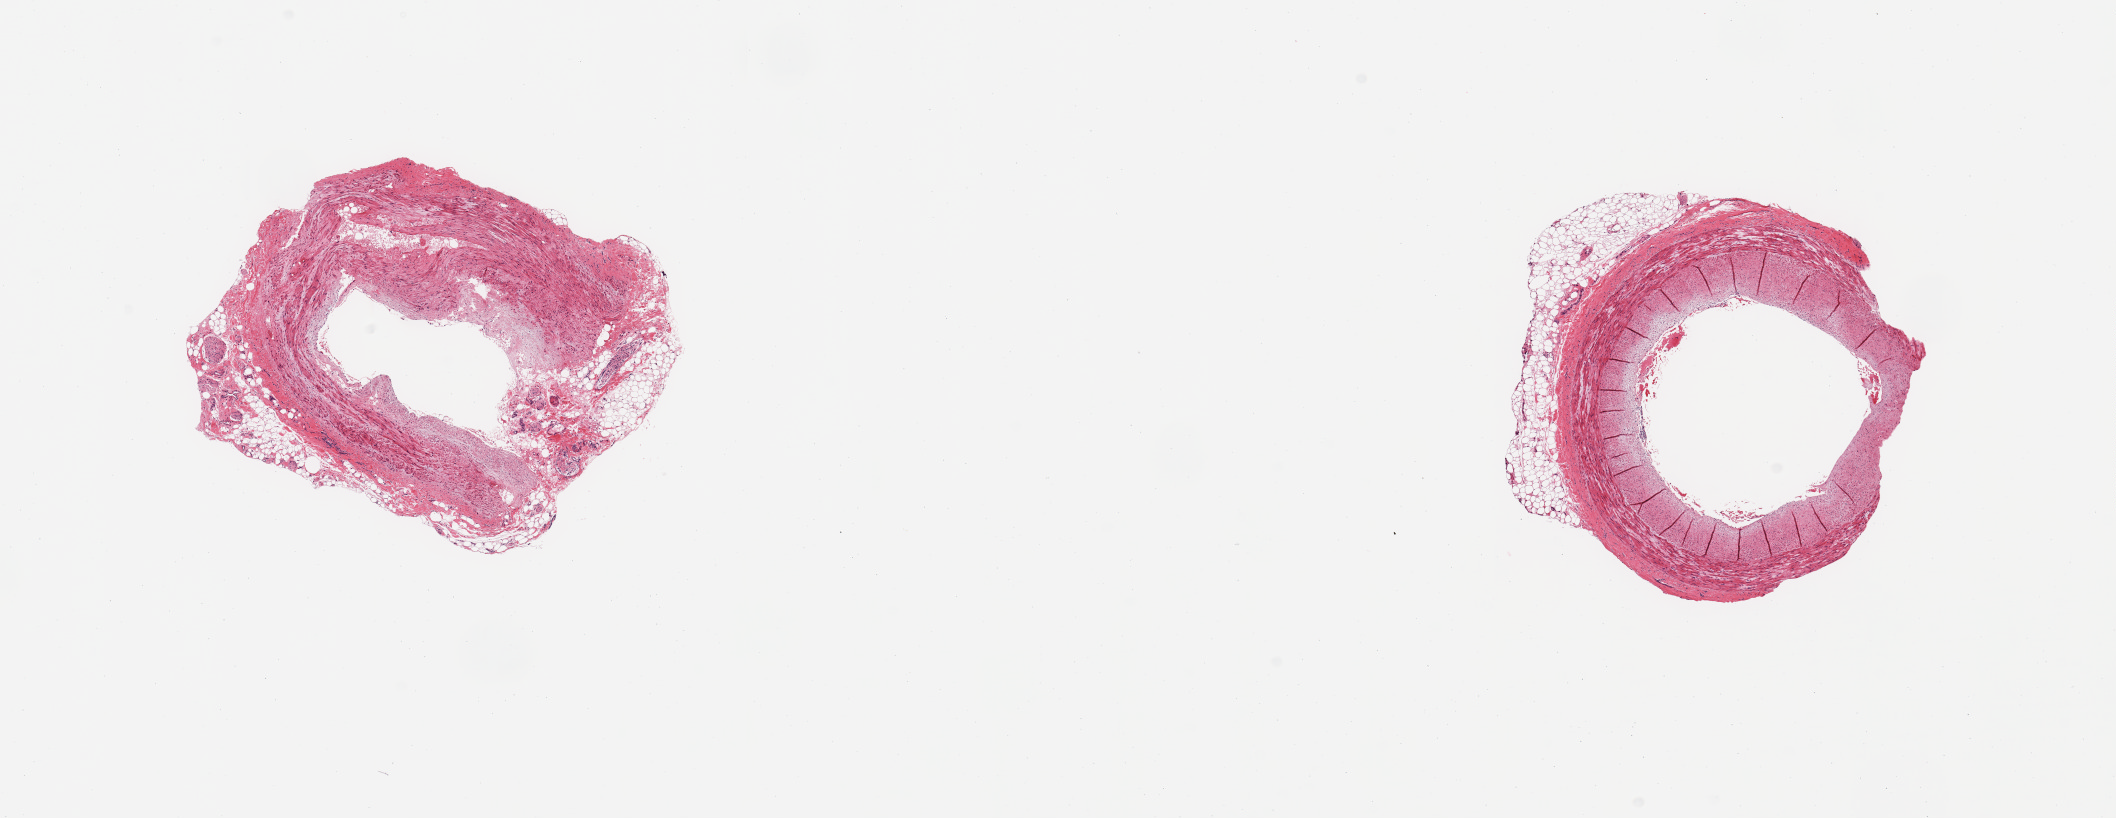
Whole-slide image, haematoxylin and eosin stain, brightfield — a low-resolution overview of the entire scanned area, about 16.7 x 6.5 mm (from a 20x scan). PAXgene-fixed, paraffin-embedded tissue. Sampled site (target tissue): coronary artery. Donor tissue sample. Donor: female.
Pathologist's review note for this sample: 2 pieces; ~0.6mm of attached adventitia; partial mild plaque in 1.